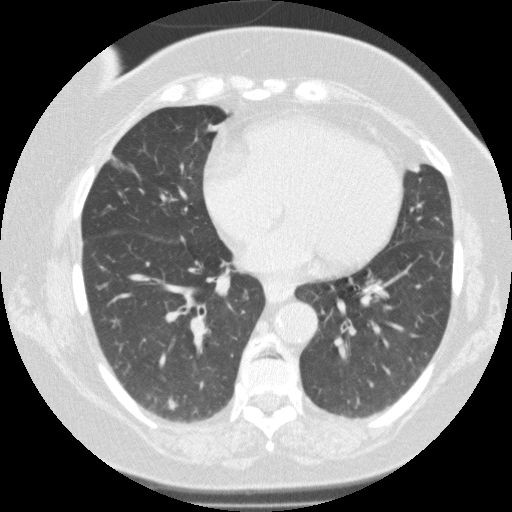
Low-dose screening chest CT, one axial slice; reconstruction kernel FC01; 120 kVp; lung window (W 1500 / L -600 HU); 2 mm slice thickness; 512 × 512 image matrix, field of view 330 × 330 mm.
Structures marked on this image (manually delineated by an expert):
- lesion 1 (nodule, lower lobe of right lung): box from (x=167, y=397) to (x=178, y=410) px